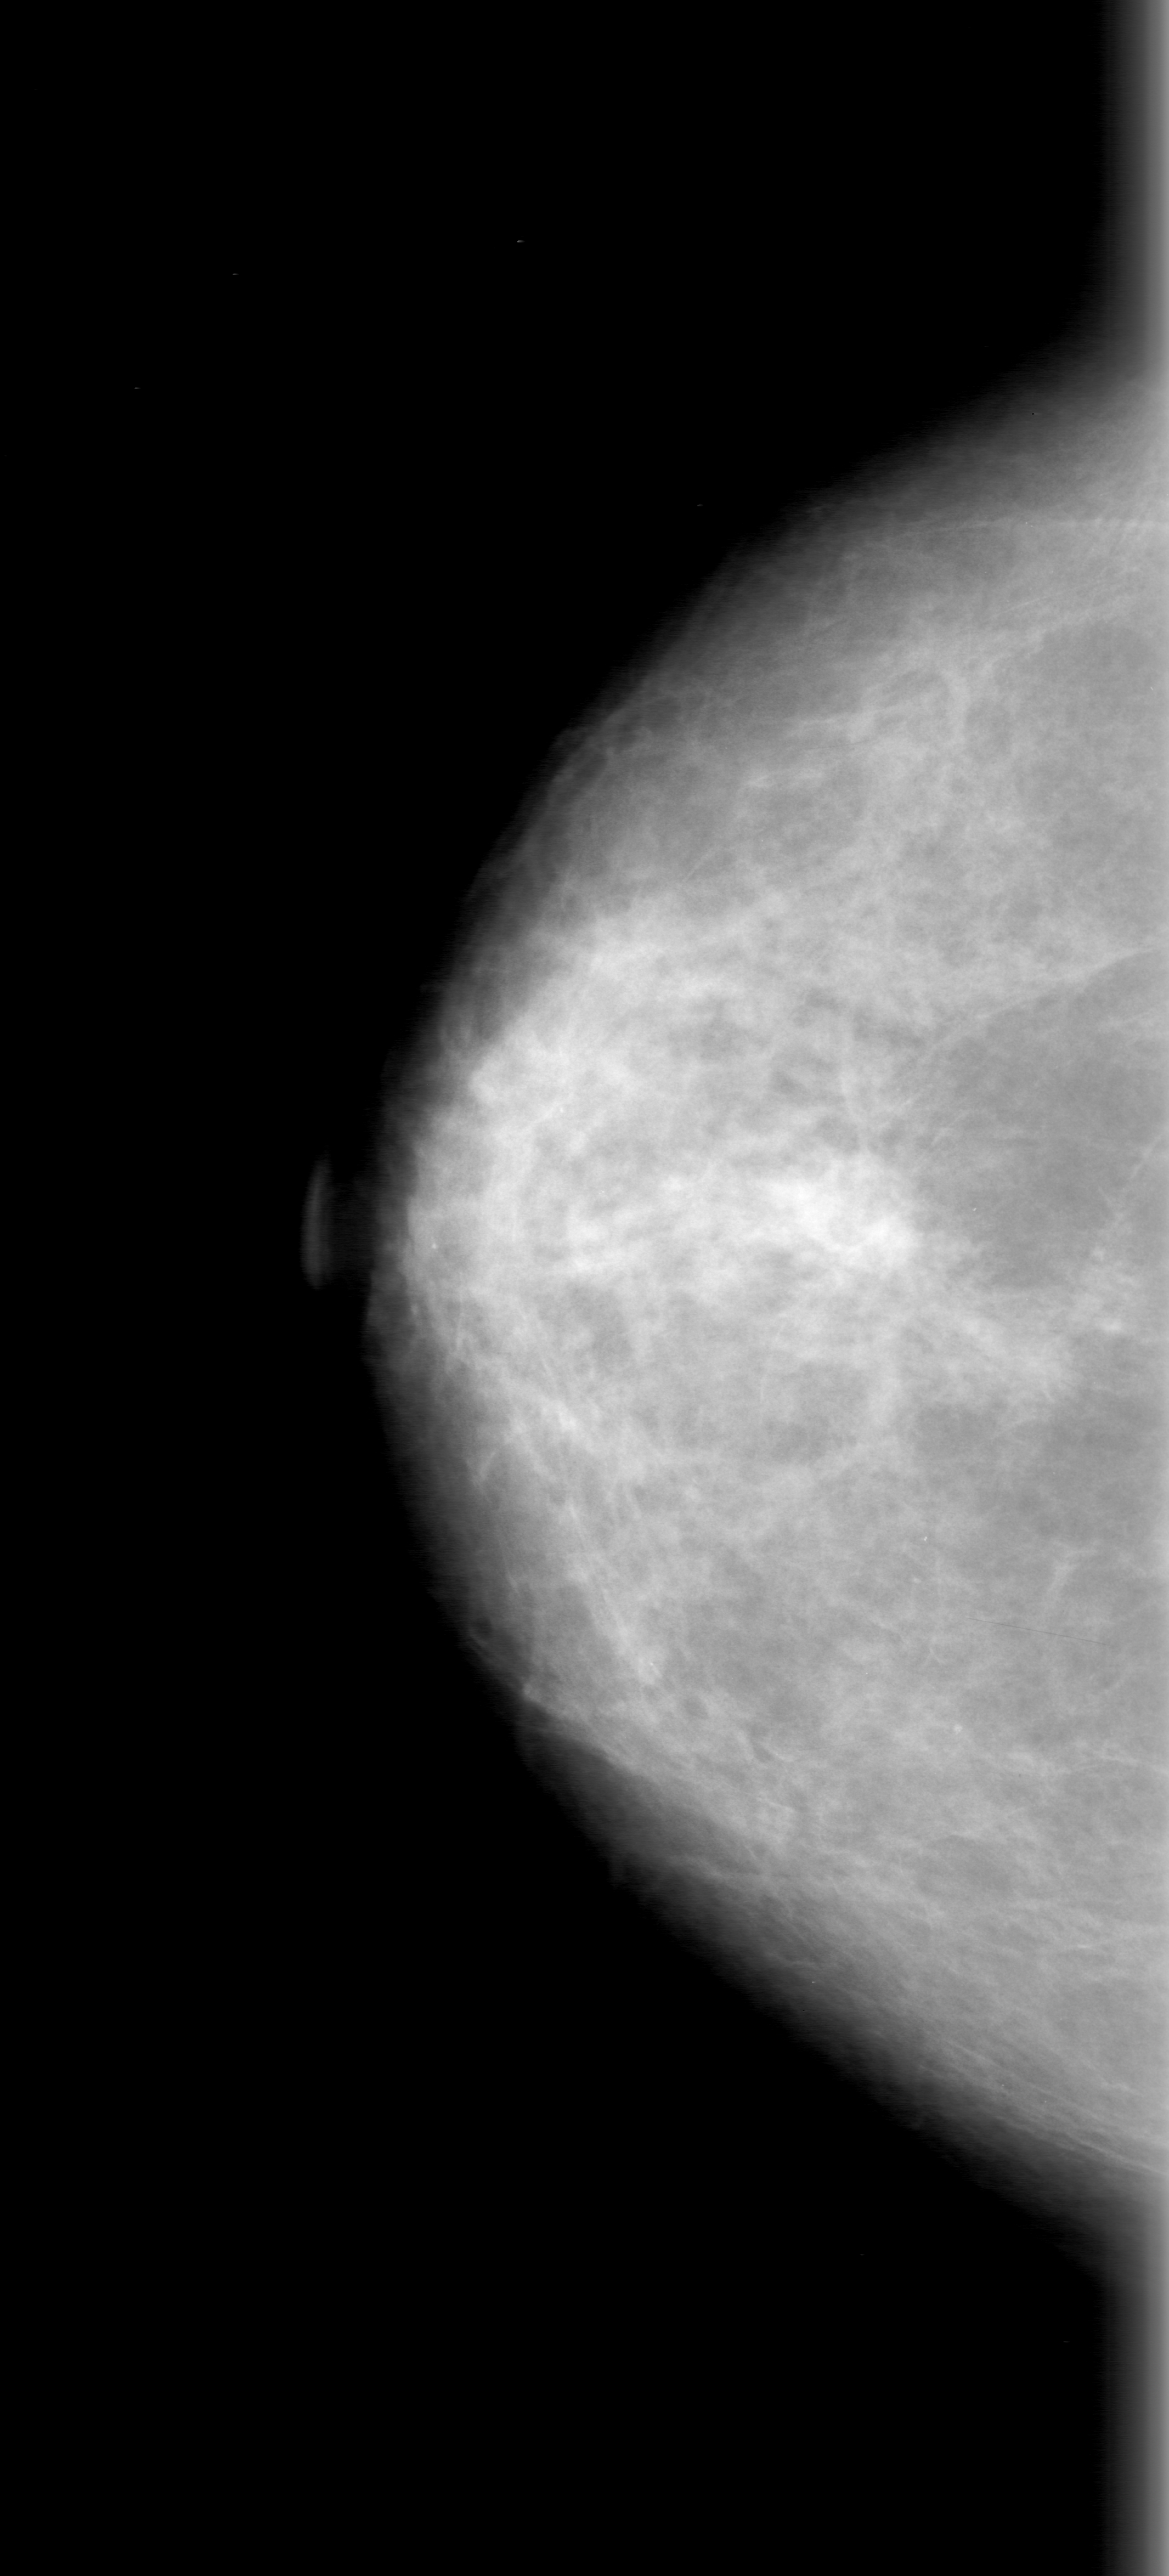
Scanned film-screen mammogram. Right breast. Craniocaudal (CC) view. Breast composition: scattered fibroglandular densities (BI-RADS density category 2 of 4). 1169 × 2576 image matrix.
Expert-marked regions of interest on this film, with their recorded descriptors:
- mass, shape oval, margins obscured; BI-RADS assessment category 0; subtlety rating 5 on a 1 (subtle) to 5 (obvious) scale; pathology (as recorded): malignant: box from (x=1104, y=1462) to (x=1169, y=1615) px